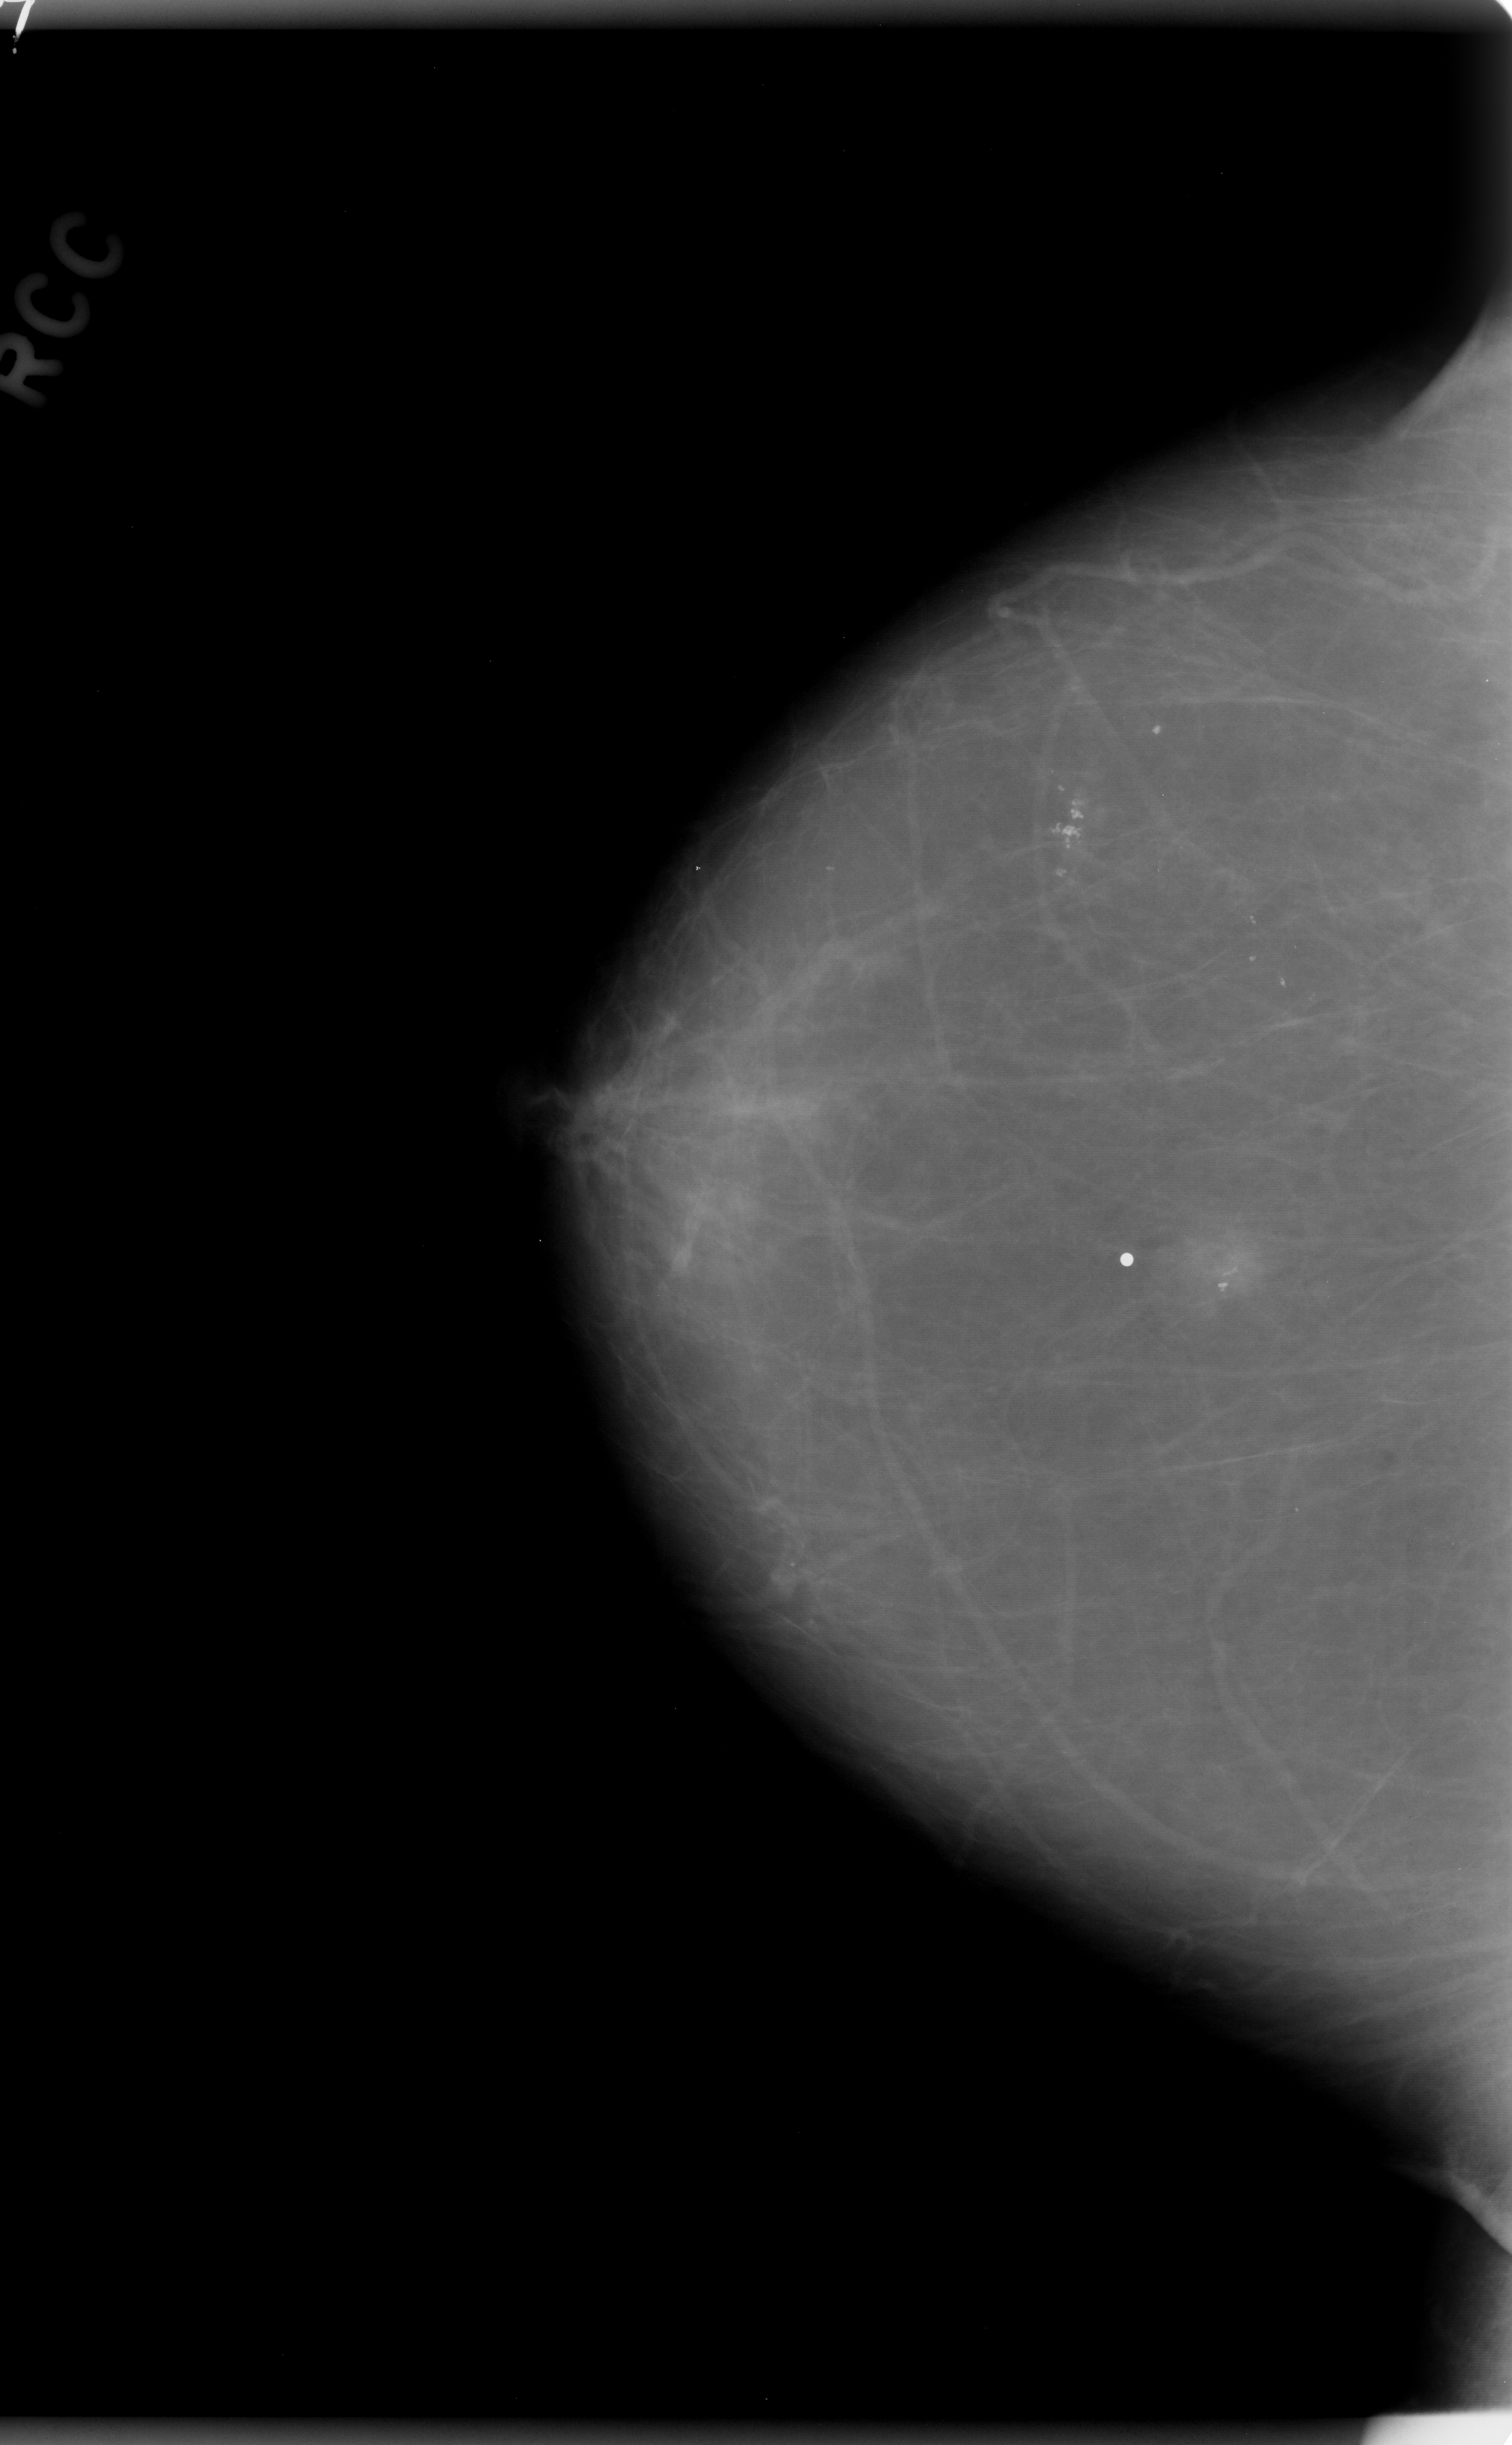
Digitized screen-film mammogram. Right breast. Craniocaudal (CC) view. Breast composition: almost entirely fatty (BI-RADS density category 1 of 4). 1512 × 2445 image matrix.
Expert-marked regions of interest on this film, with their recorded descriptors:
- Finding 1 of 3: calcifications, morphology pleomorphic, distribution clustered; BI-RADS assessment category 4; subtlety rating 5 on a 1 (subtle) to 5 (obvious) scale; pathology result (as recorded, not read from the image): benign: box from (x=979, y=744) to (x=1146, y=921) px
- Finding 2 of 3: calcifications, morphology fine linear branching, distribution clustered; BI-RADS assessment category 4; pathology (as recorded): benign: (x=1101, y=1154)–(x=1298, y=1361)
- Finding 3 of 3: calcifications, morphology punctate, distribution clustered; BI-RADS assessment category 4; pathology (as recorded): benign: (x=1177, y=870)–(x=1361, y=1070)